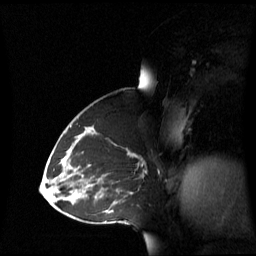
Breast MRI (dynamic contrast-enhanced), one sagittal slice; slice 35 of 60 in the series (ordered by position); dynamic contrast-enhanced series, image 2 of 3 at this slice position (ordered by acquisition); 1.5 T; TE 4.2 ms, TR 8.4 ms; 2.8 mm slice thickness; 256 × 256 image matrix, field of view 270 × 270 mm. Patient: female, 43 years. Case-level facts recorded for this patient, not image findings: setting: breast cancer imaged before/during neoadjuvant chemotherapy; receptor status: triple-negative.
Structures marked on this image (semi-automatic segmentation, software-assisted and operator-edited):
- analysis volume of interest (the breast-tissue region the enhancement analysis was run in; not a lesion): bounding box <69,137,143,198> (left, top, right, bottom; pixels)
- tumour enhancement mask (voxels above the 70 % enhancement threshold inside the analysis volume of interest): <128,150,136,156>